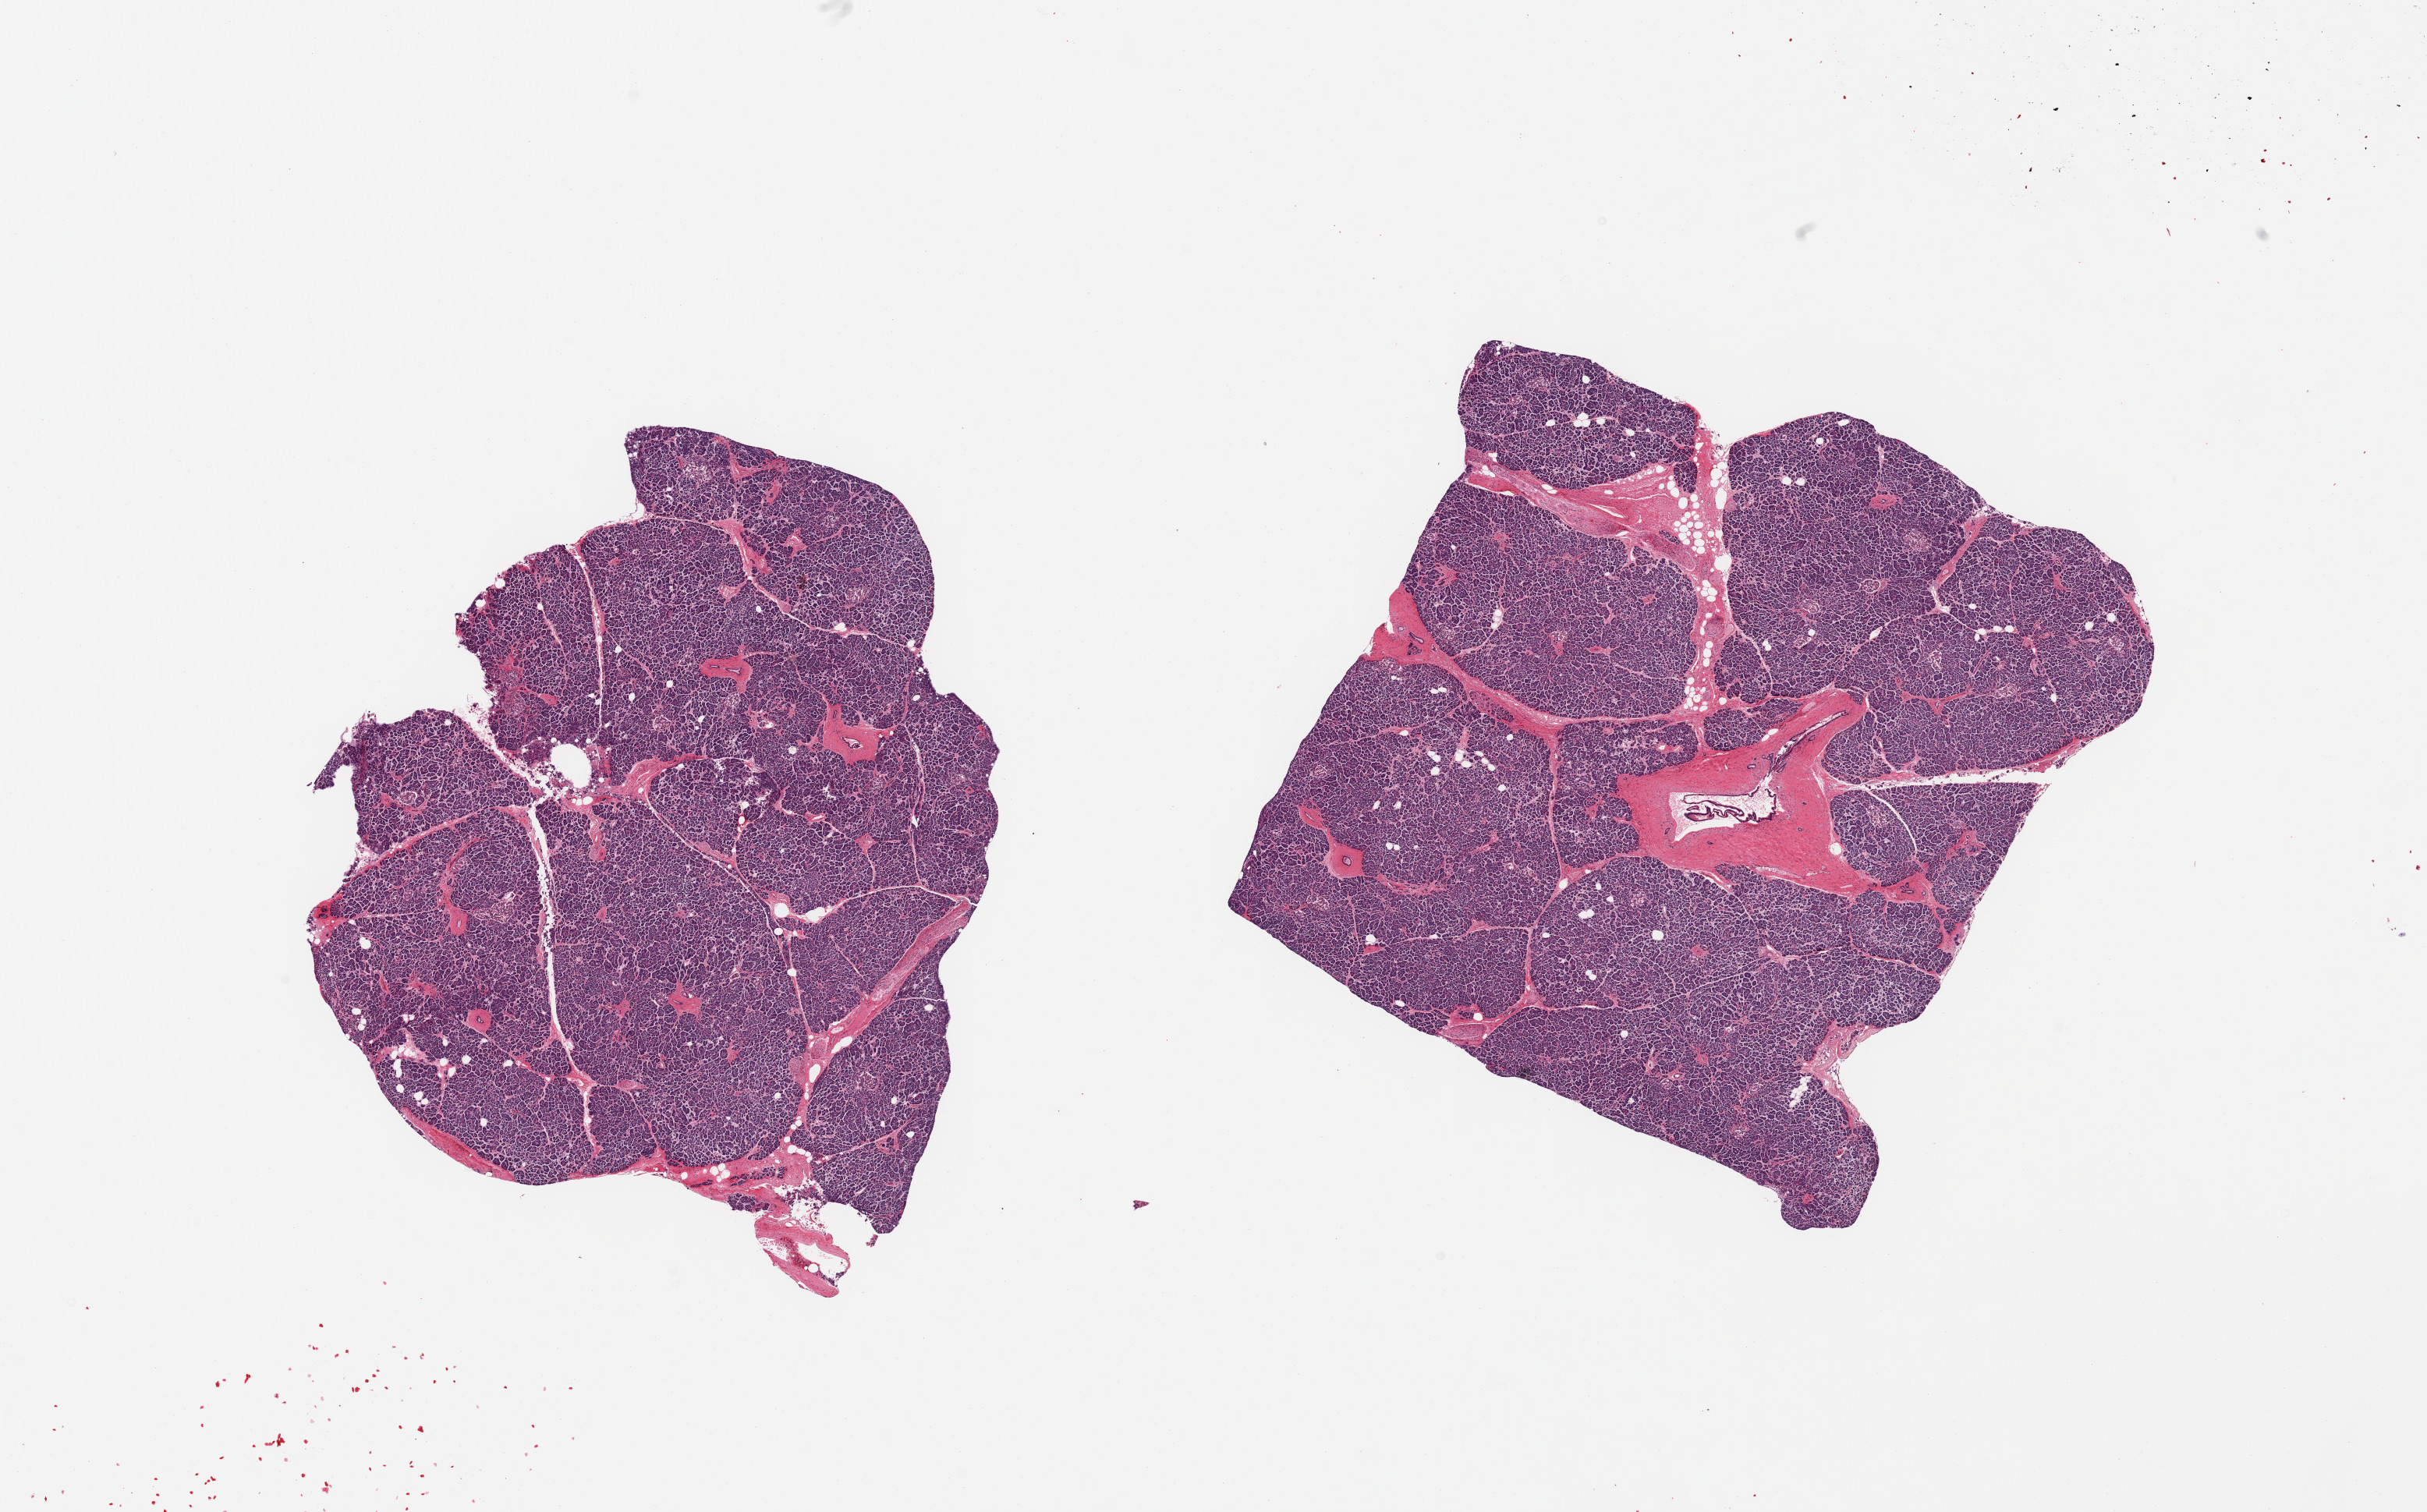
Haematoxylin and eosin whole-slide image, whole scanned area (about 24.6 x 15.3 mm) shown as a low-resolution overview; PAXgene-fixed, paraffin-embedded tissue; target tissue: pancreas; tissue donor sample. Donor: male.
Pathologist's review note for this sample: 2 pieces; well dissected.